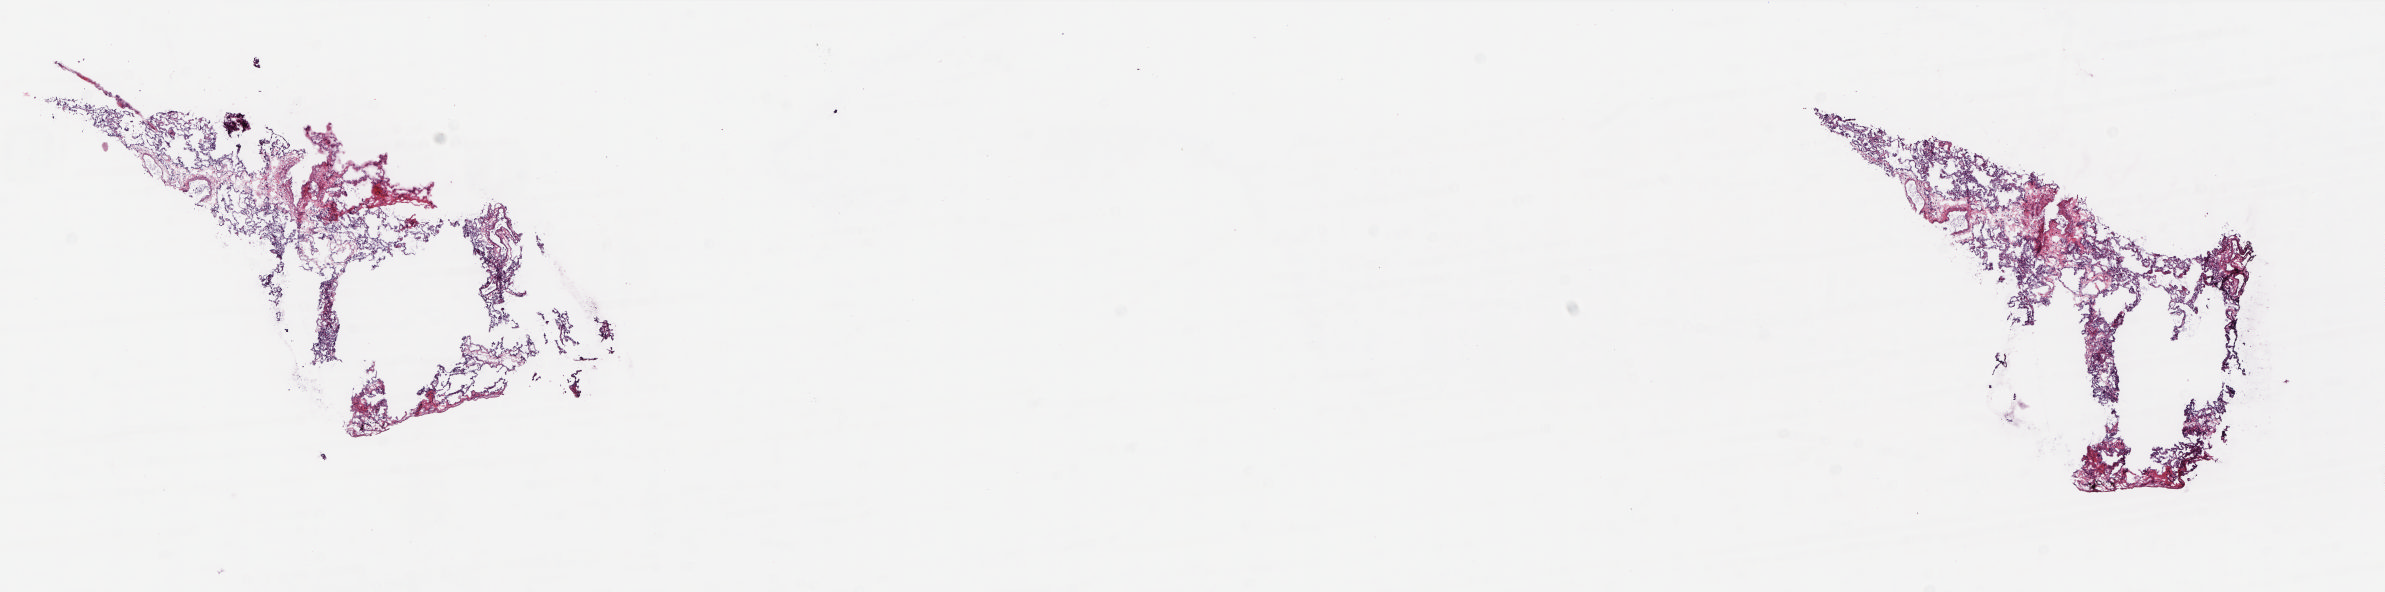
Hematoxylin and eosin (H&E) stained whole-slide image, a low-resolution overview of the entire scanned area, about 19.2 x 4.8 mm. Frozen section from the top of the tissue portion. Solid tissue normal (non-tumour tissue) sample from the lung. Female, age 67 years at initial diagnosis. Pathologist review of this section (percent, as recorded): tumour cells 0%, tumour nuclei 0%, normal cells 100%, stromal cells 0%, necrosis 0%. Infiltration values recorded for this section: lymphocyte infiltration 2%, monocyte infiltration 5%, neutrophil infiltration 0%.
This section: solid tissue normal (non-tumour) sample from the same patient. Patient diagnosis: Adenocarcinoma, NOS.